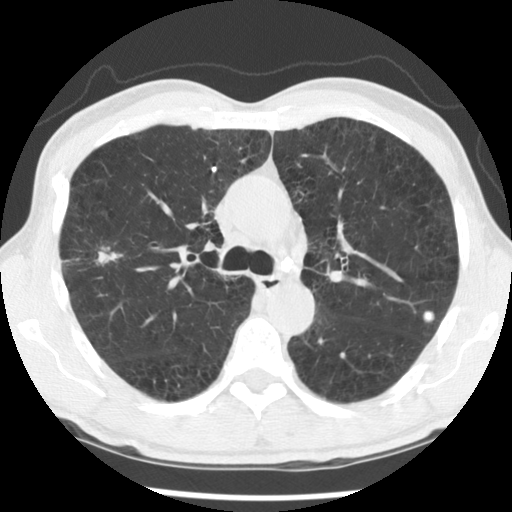
Low-dose screening chest CT, axial slice. Second annual screen. Lung window (W 1500 / L -600 HU). 2.5 mm slice thickness. Standard (soft-tissue) reconstruction kernel (STANDARD). Slice 86 of 138 in the series. 512 × 512 image matrix. Male participant, aged 56 years at enrolment. Current smoker at enrolment.
Lesion marked by an expert reader, bounding box <51,232,137,291> (left, top, right, bottom; pixels). Reader record for this screening exam (exam-level; its link to the box is not recorded): non-calcified nodule or mass ≥4 mm, right upper lobe, 30 × 18 mm, spiculated (stellate) margins, mixed attenuation, pre-existing on the prior screen: yes; interval growth: yes. Participant outcome: lung cancer diagnosed 326 days after this screen — squamous cell carcinoma, NOS, right upper lobe, right middle lobe, moderately differentiated (G2), stage IB (AJCC 6th edition), 70 mm at pathology.